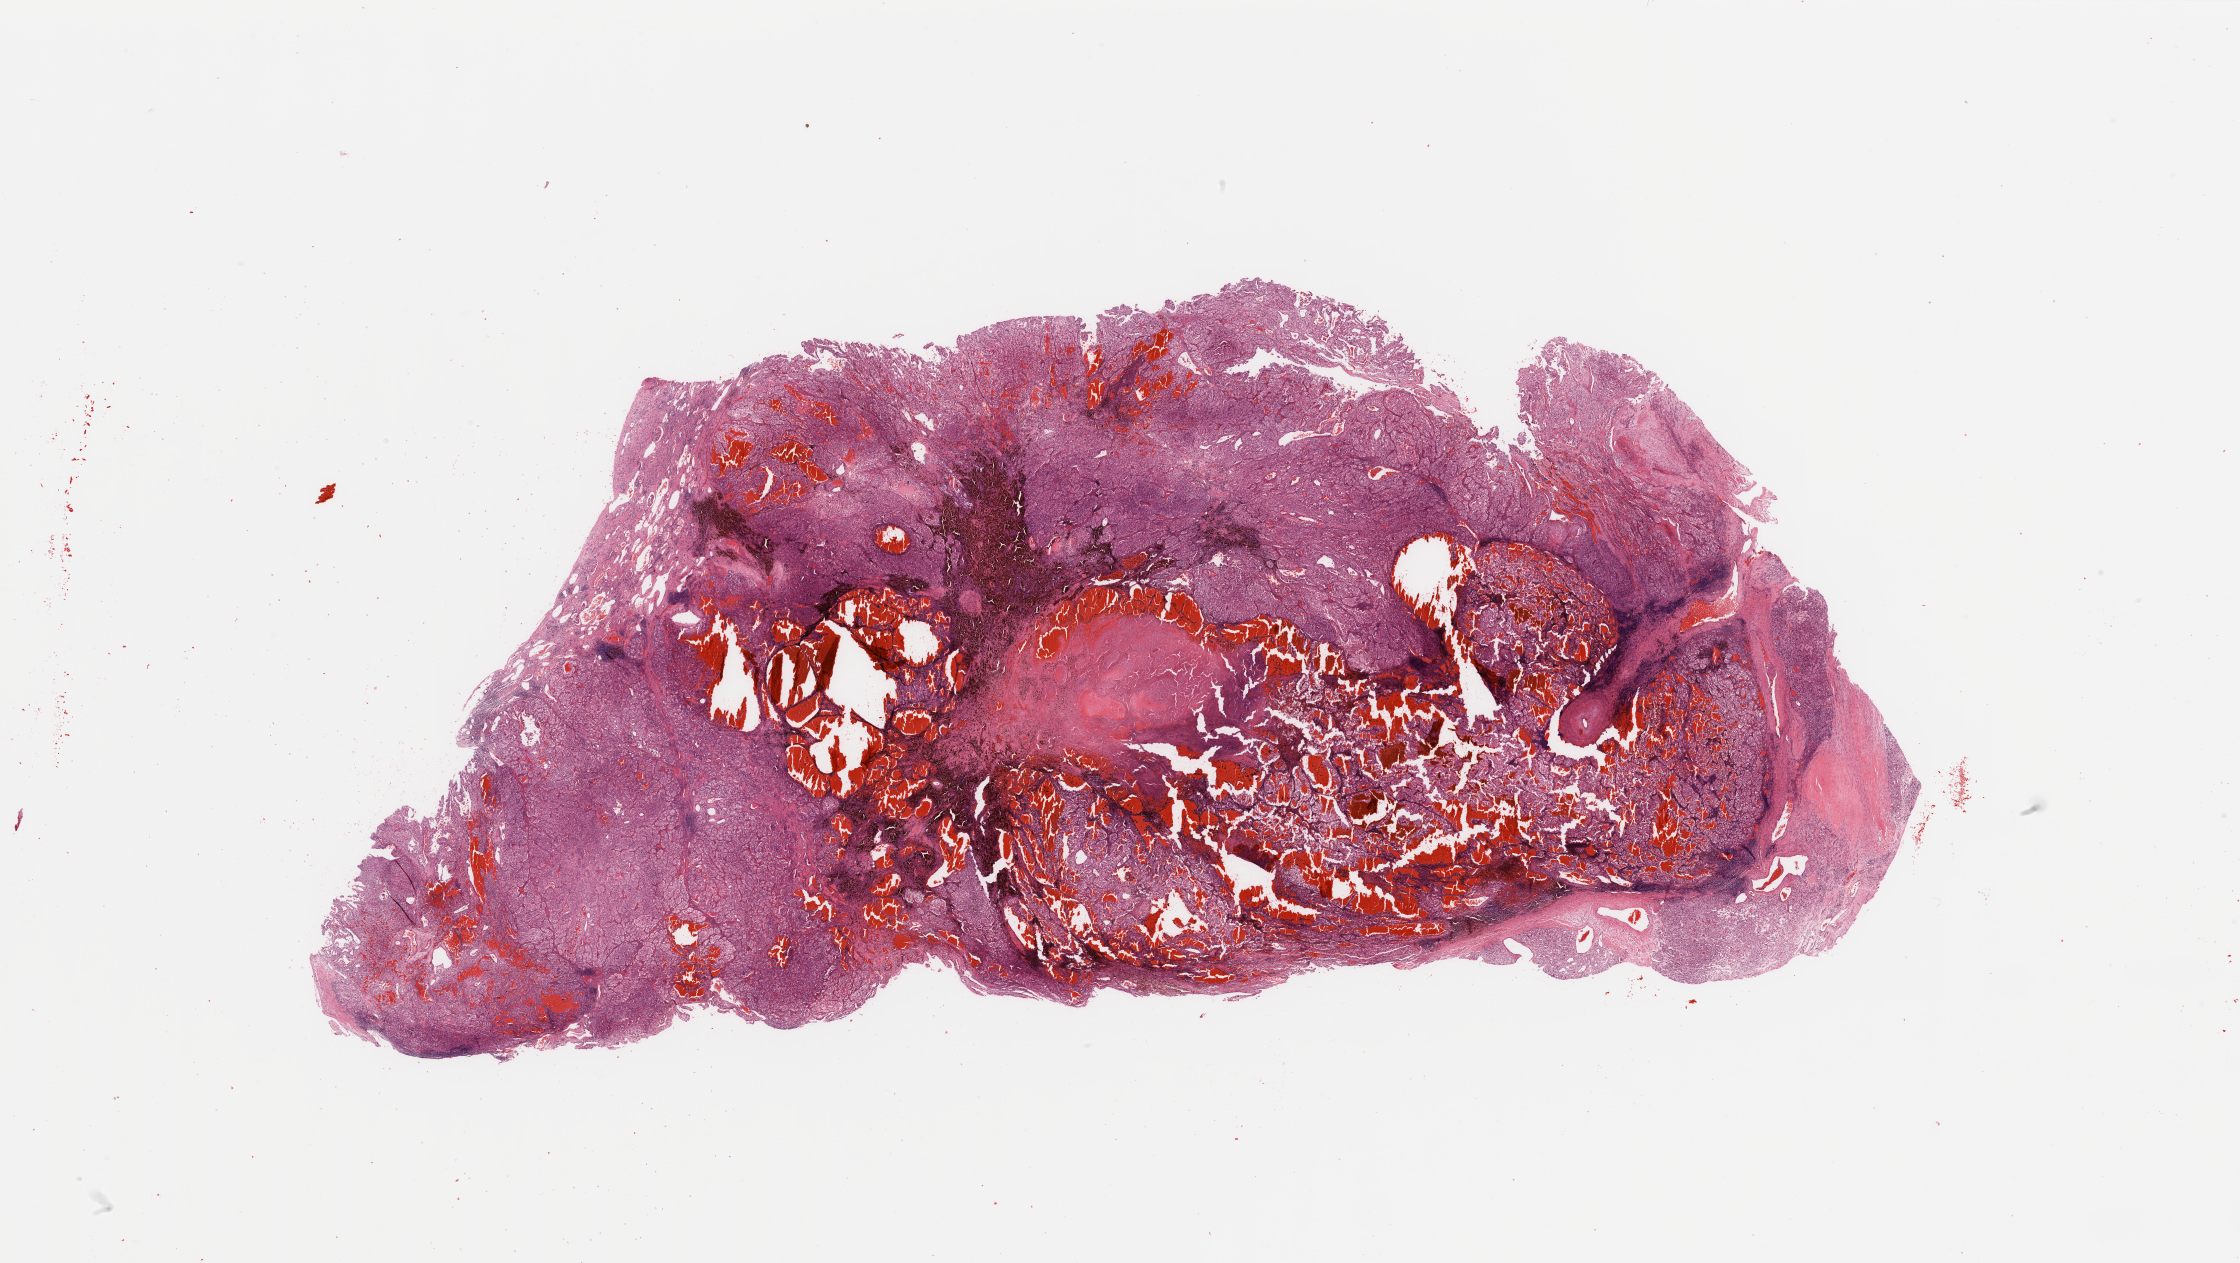
Digitized H&E tissue section (whole slide), low-resolution overview of the scanned area, about 35.4 x 20.0 mm. Tumour tissue sample, kidney. Male, 53 y/o. Histologic grade: G3 (poorly differentiated).
* histologic diagnosis: Renal cell carcinoma, NOS